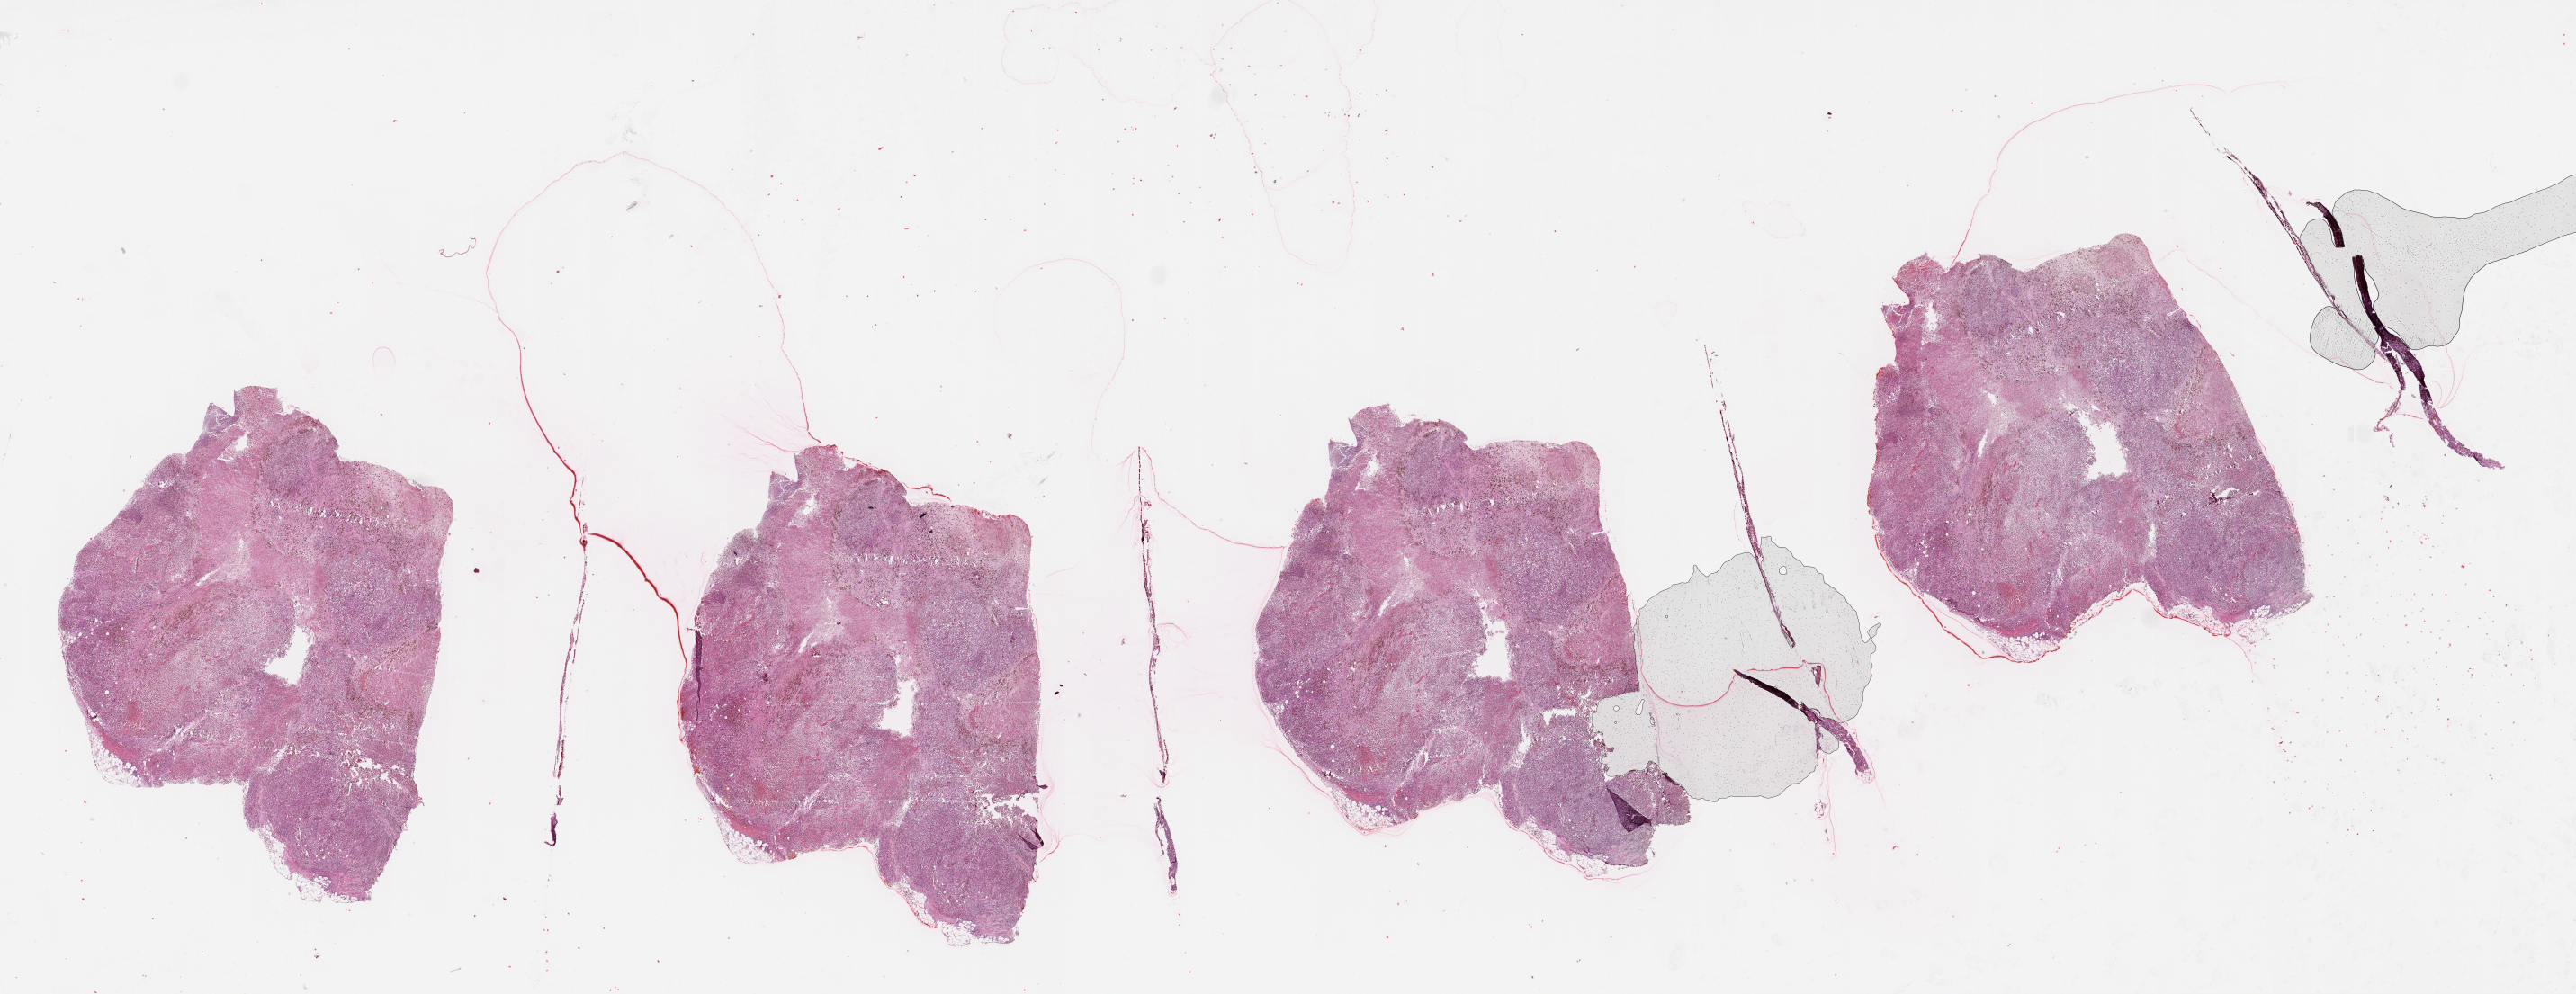
Whole-slide histology image, H&E — a low-resolution overview of the entire scanned area, about 46.1 x 17.8 mm. 76-year-old female patient.
- patient diagnosis: Malignant melanoma, NOS